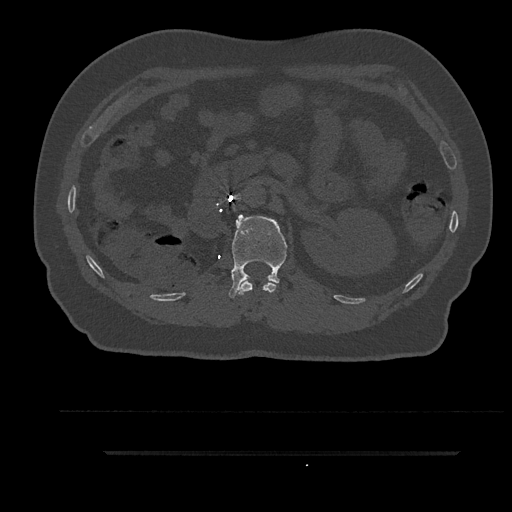
CT including the spine, one axial slice. Position 193 of 797 along the scan axis. 120 kVp. Bone window (W 1800 / L 400 HU). 512 × 512 image matrix, field of view 432 × 432 mm. Male patient, age 63 years. Case-level facts recorded for this patient, not image findings: primary cancer: renal.
Structures marked on this image (semi-automatic segmentation, software-assisted and operator-edited):
- L1 vertebra: bounding box (x1, y1, x2, y2) in pixels: (228, 214, 288, 298)
- T12 vertebra: (239, 280, 277, 295)